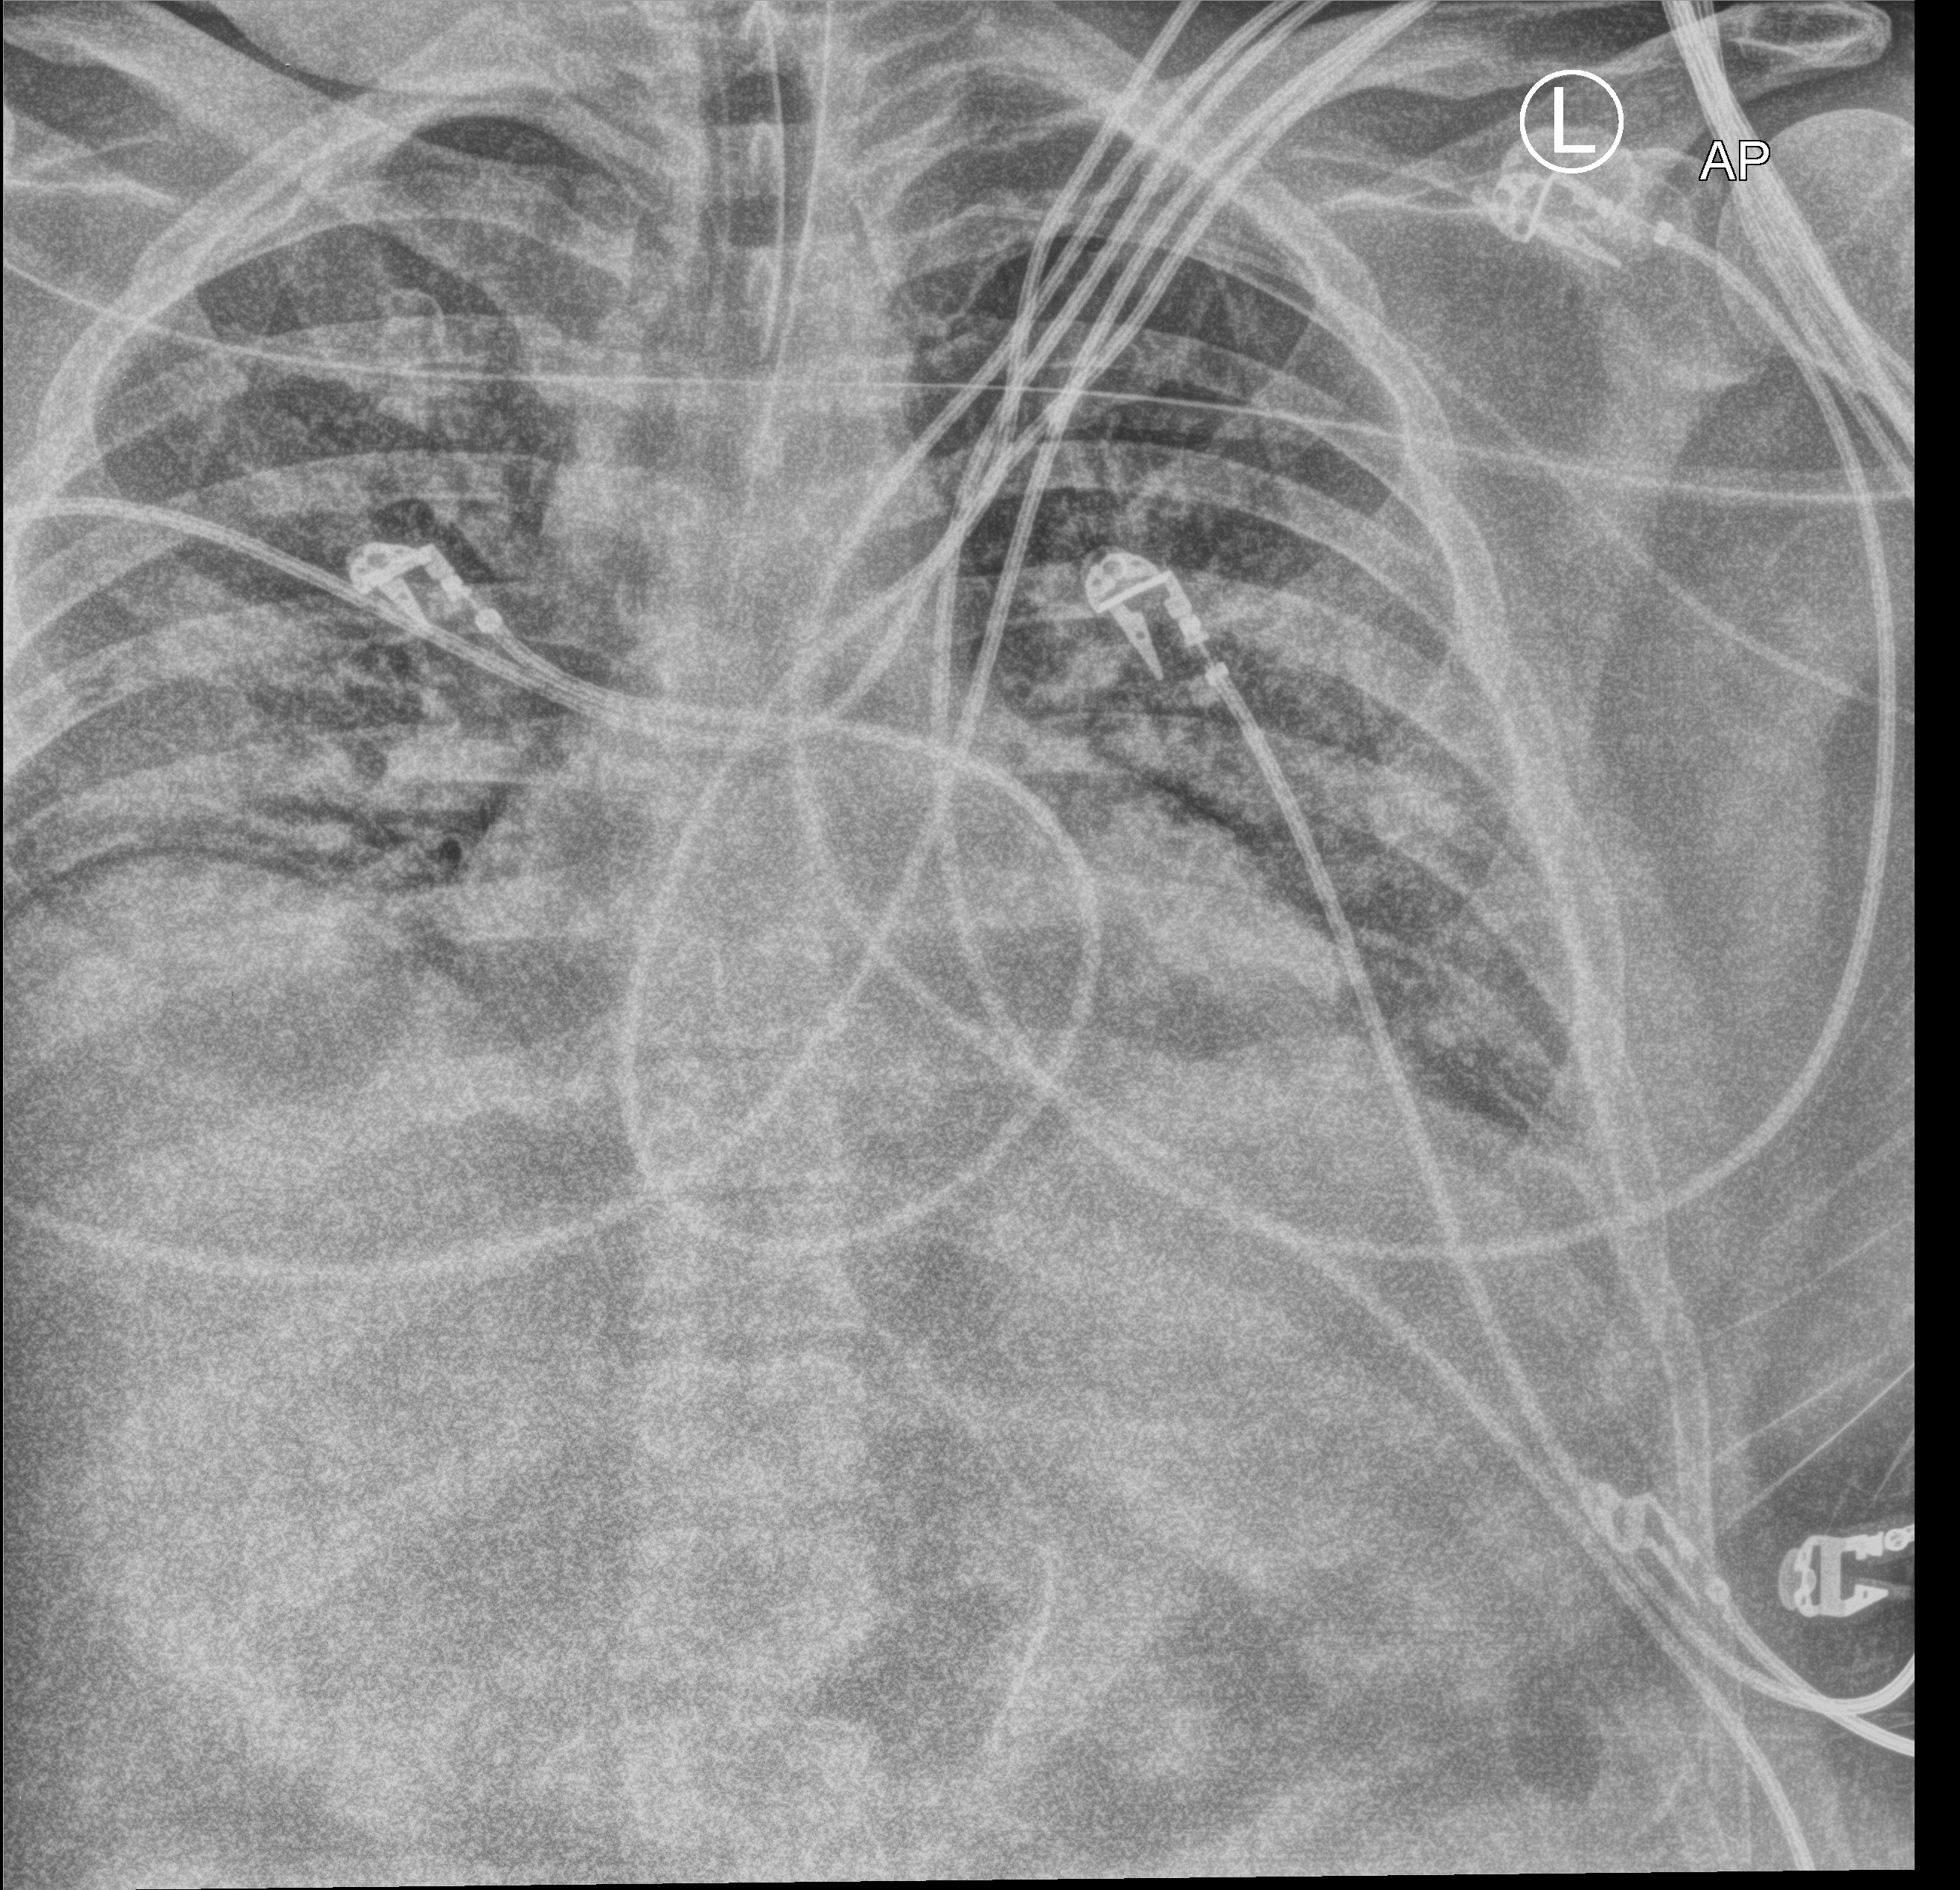
Bedside chest radiograph (computed radiography), anteroposterior (AP) projection. Patient hospitalised with COVID-19; male, aged 18–59 years.
Admission-level facts for this patient (not findings on this image; timing relative to this image not recorded): mechanically ventilated during this hospital stay: yes; diabetes (admission record): no.